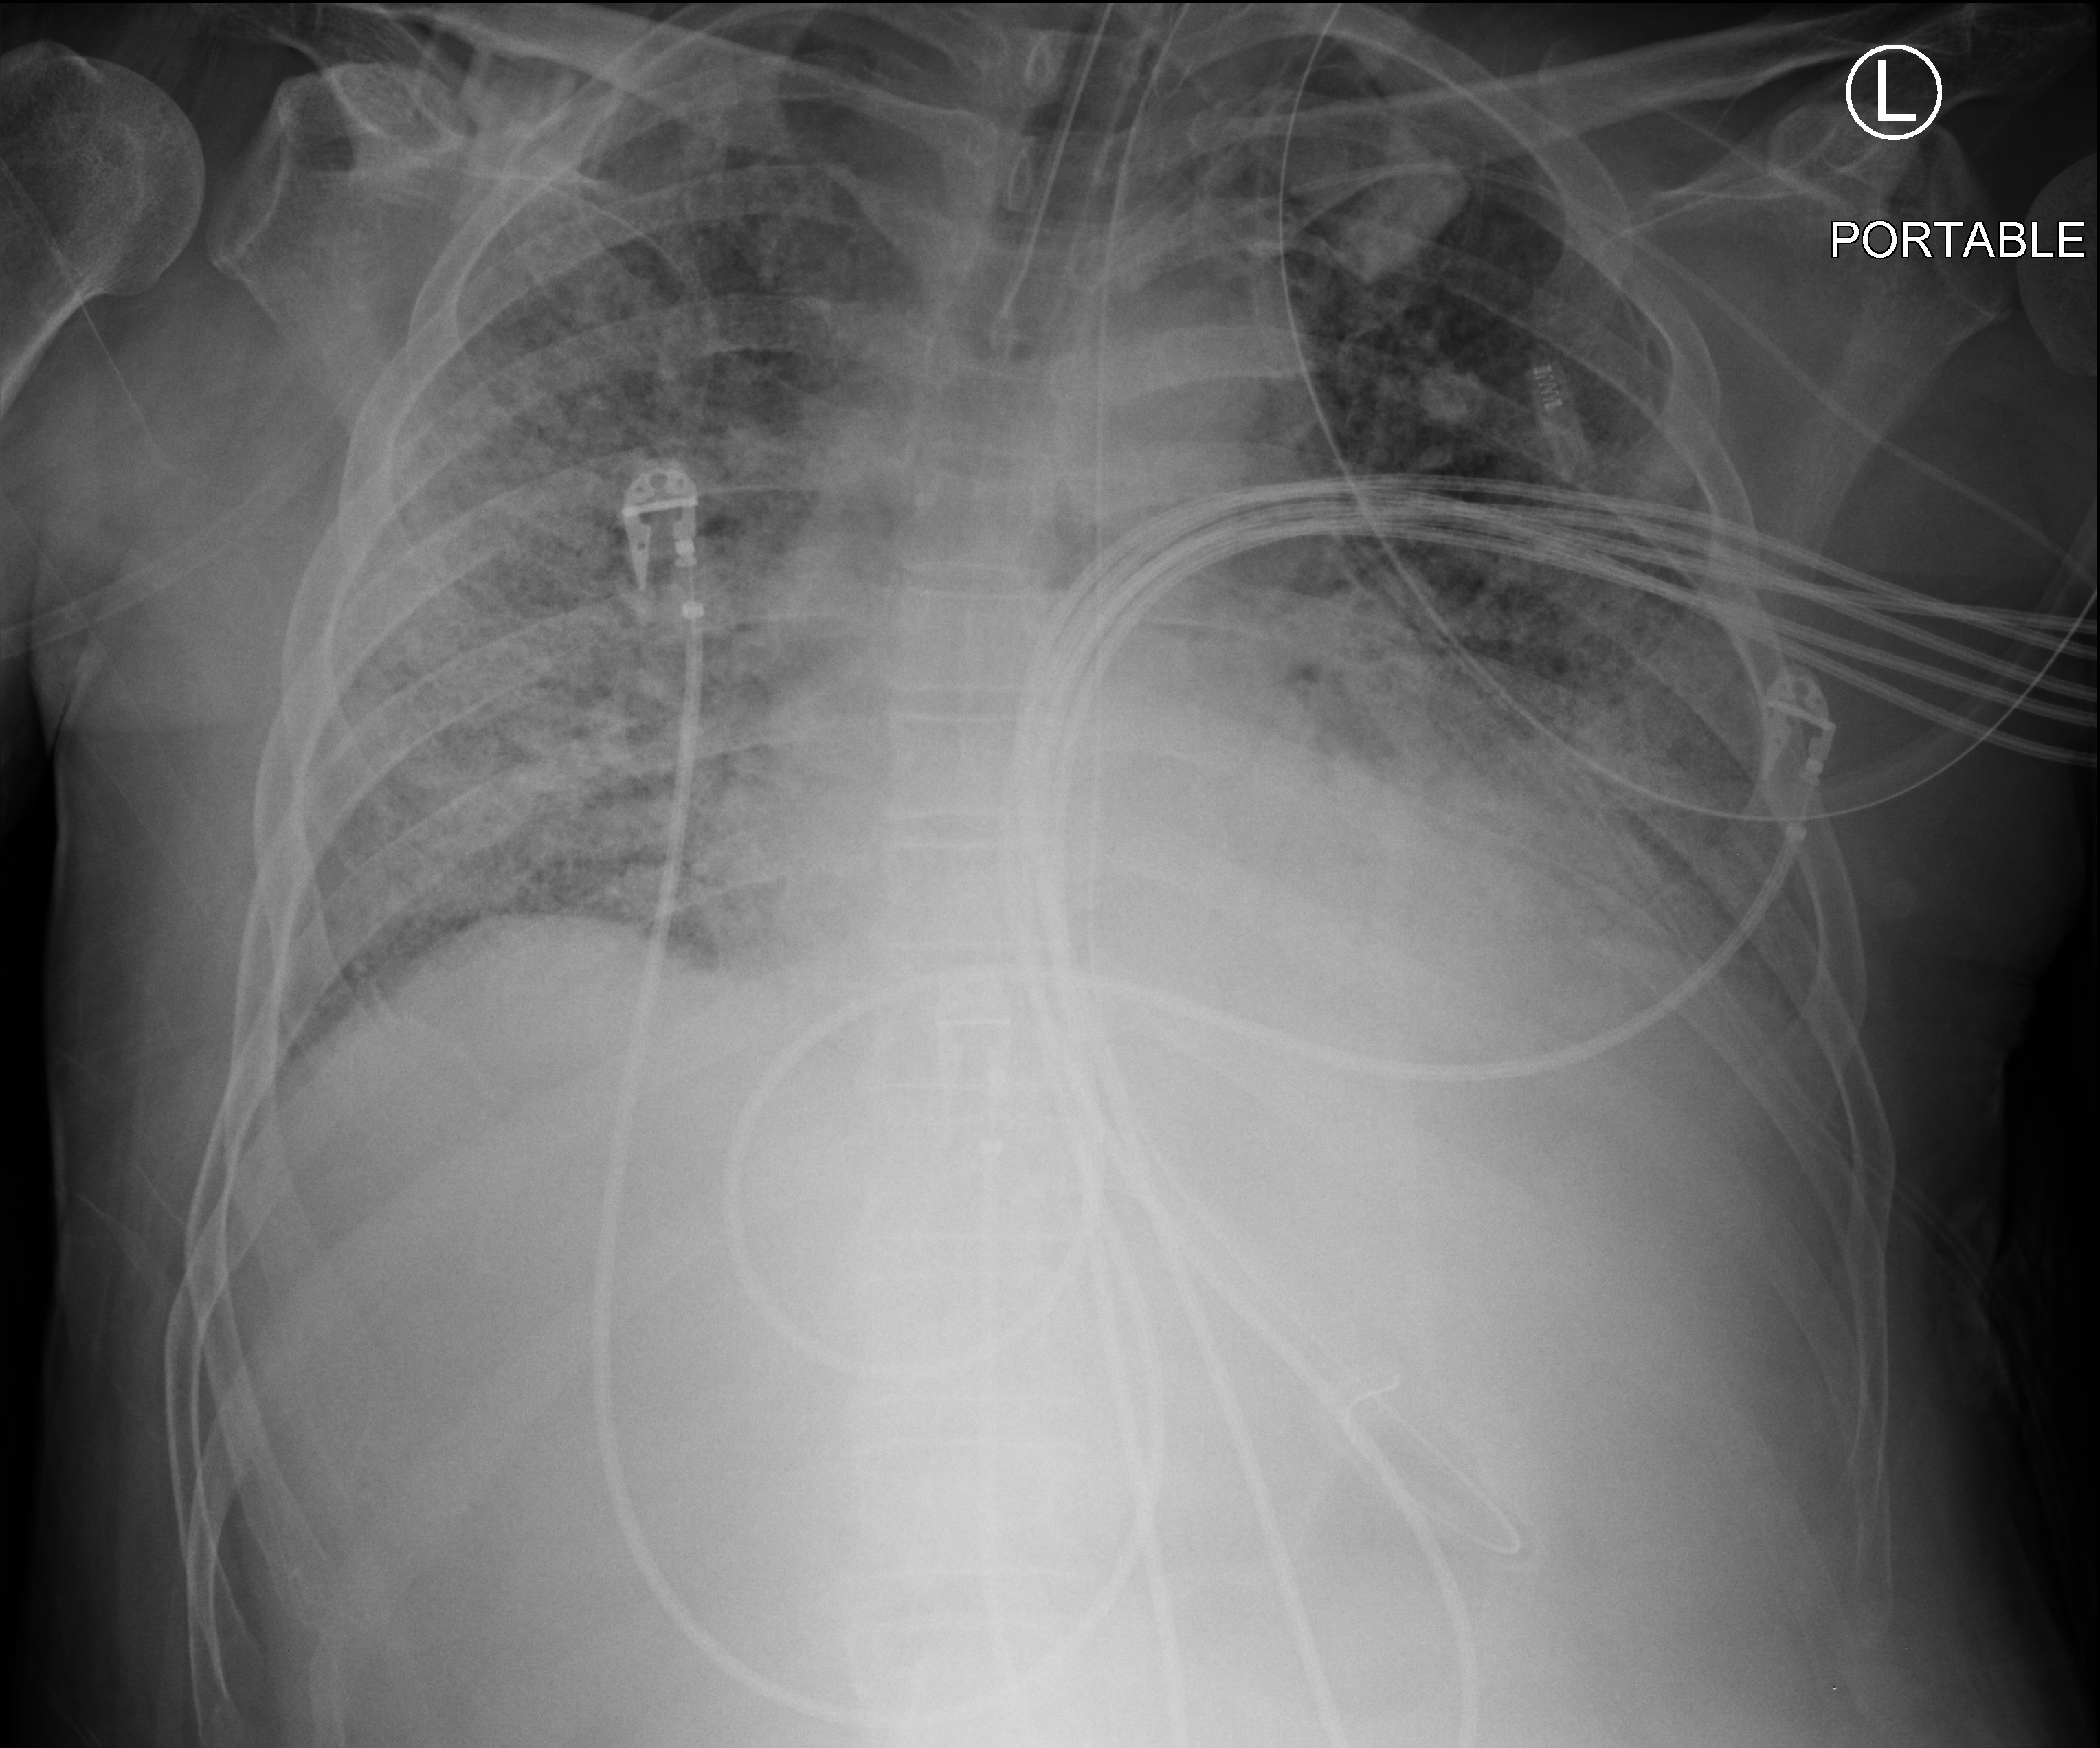
Portable chest radiograph; anteroposterior (AP) projection. Patient hospitalised with COVID-19; male, aged 60–74 years.
From the hospital-stay record, not from the radiograph (when in the stay this image was taken is not recorded):
- mechanically ventilated during this hospital stay: yes
- admitted to intensive care during this hospital stay: yes